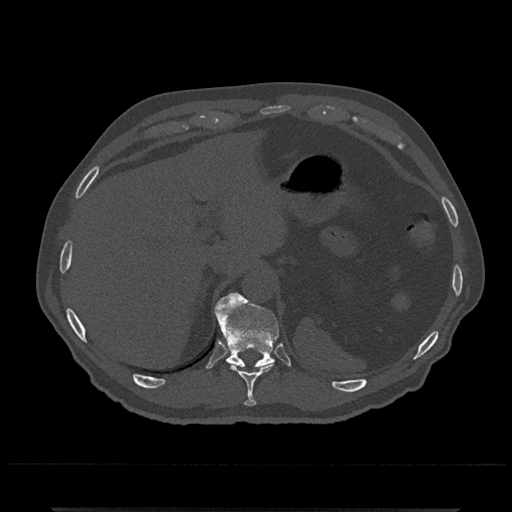
CT including the spine, one axial slice. Slice 523 of 797 in the series (ordered by position). 120 kVp. Bone window (W 1800 / L 400 HU). 0.5 mm slice thickness. 512 × 512 image matrix, field of view 393 × 393 mm. Patient: male, 67 years. Case-level facts recorded for this patient, not image findings: primary cancer: prostate.
Structures marked on this image (semi-automatic segmentation, software-assisted and operator-edited):
- T10 vertebra: bounding box [x1, y1, x2, y2] px = [233, 365, 275, 407]
- T11 vertebra: [214, 293, 279, 368]